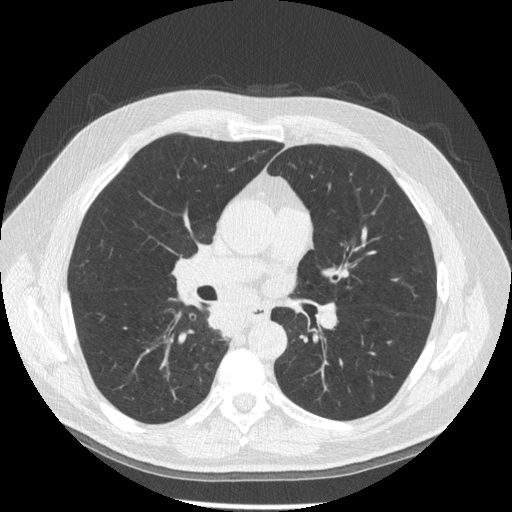
Low-dose screening chest CT, one axial slice; slice 101 of 181 in the series (ordered by position); reconstruction kernel STANDARD; 120 kVp; lung window (W 1500 / L -600 HU); 1.25 mm slice thickness; 512 × 512 image matrix, field of view 370 × 370 mm.
Annotated regions visible in this slice (outlined manually by an expert reader):
- lesion 1 (tumor, lower lobe of right lung): bounding box [x1, y1, x2, y2] px = [208, 302, 243, 336]